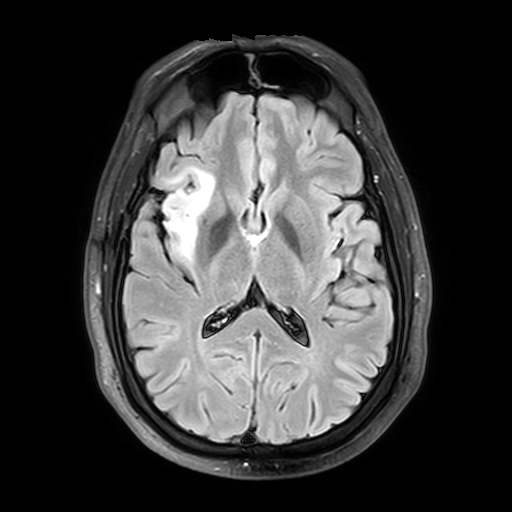
Brain MRI from a brain-tumour surgery series, one axial slice; slice 20 of 42 in the series (ordered by position); T2 FLAIR; 4 mm slice thickness; 512 × 512 image matrix. From the clinical record (not read from this slice): histopathology: Astrocytoma; WHO grade: 2; IDH mutation: yes; tumour location: Right Insular.
Annotated regions visible in this slice (expert manual segmentation):
- tumour: bounding box (x1, y1, x2, y2) in pixels: (137, 166, 223, 259)